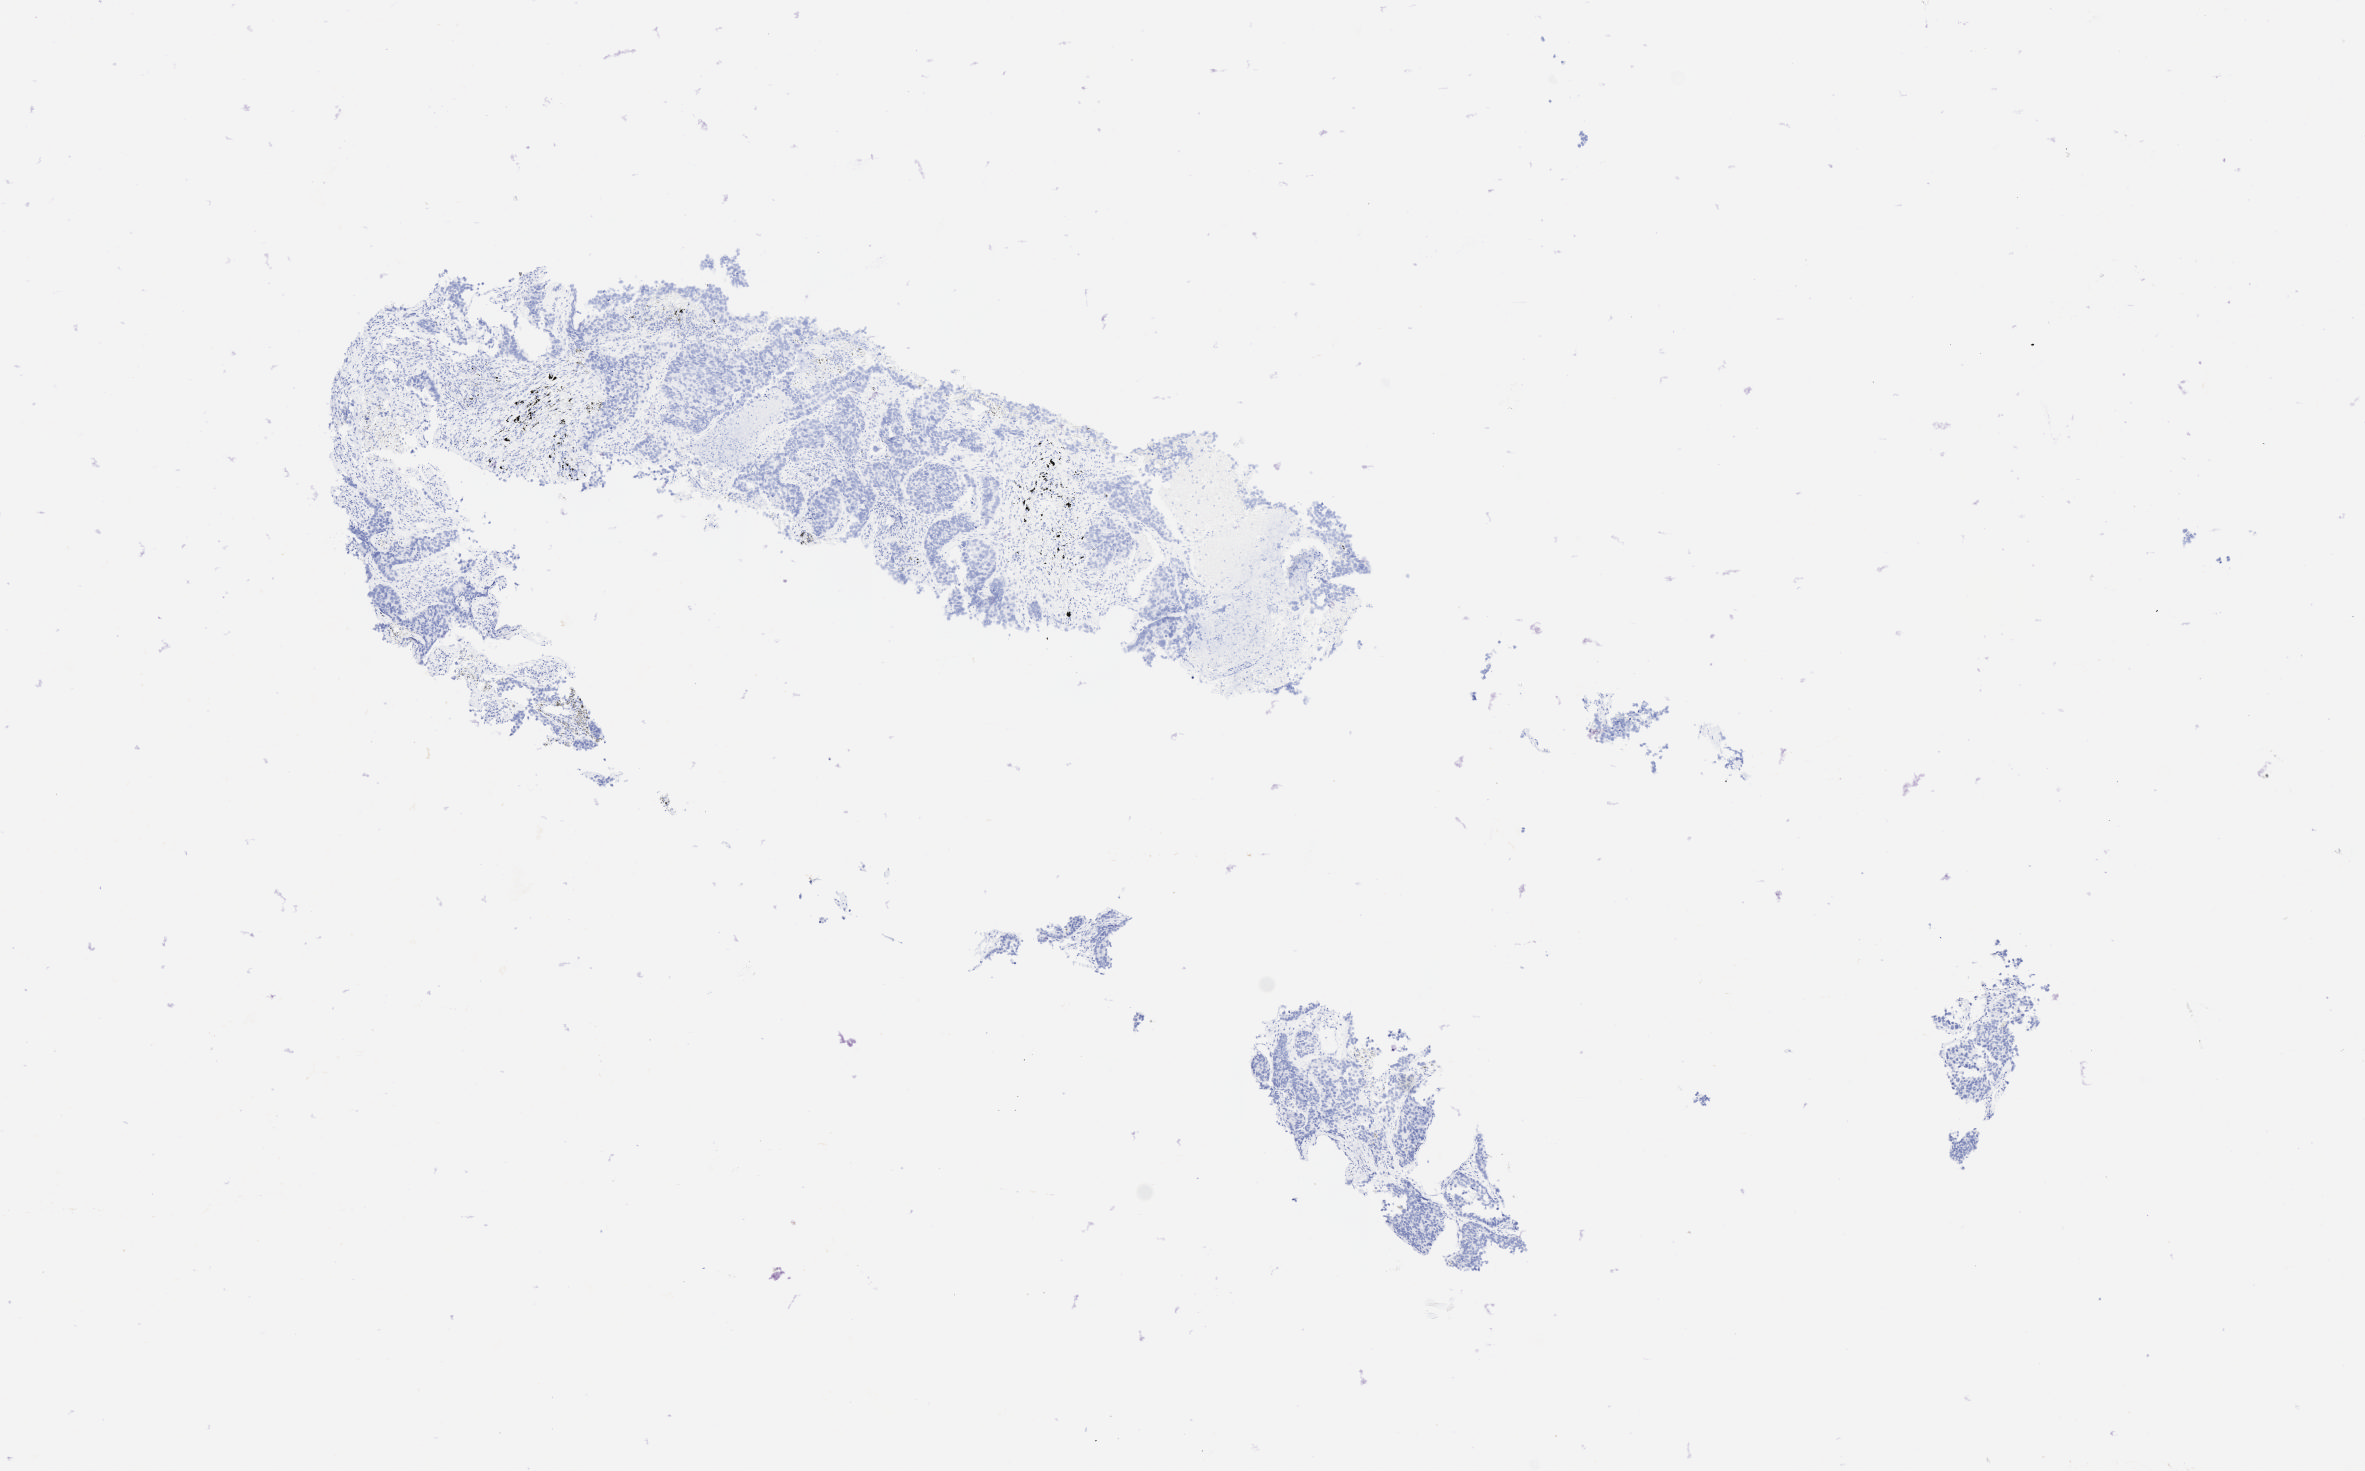
Whole-slide image, immunohistochemical stain for p40, low-resolution overview of the scanned area, about 9.6 x 5.9 mm, specimen: tumor tissue, site: lung. Male patient, 68 years old.
• histologic diagnosis: Bronchiolo-alveolar carcinoma, non-mucinous